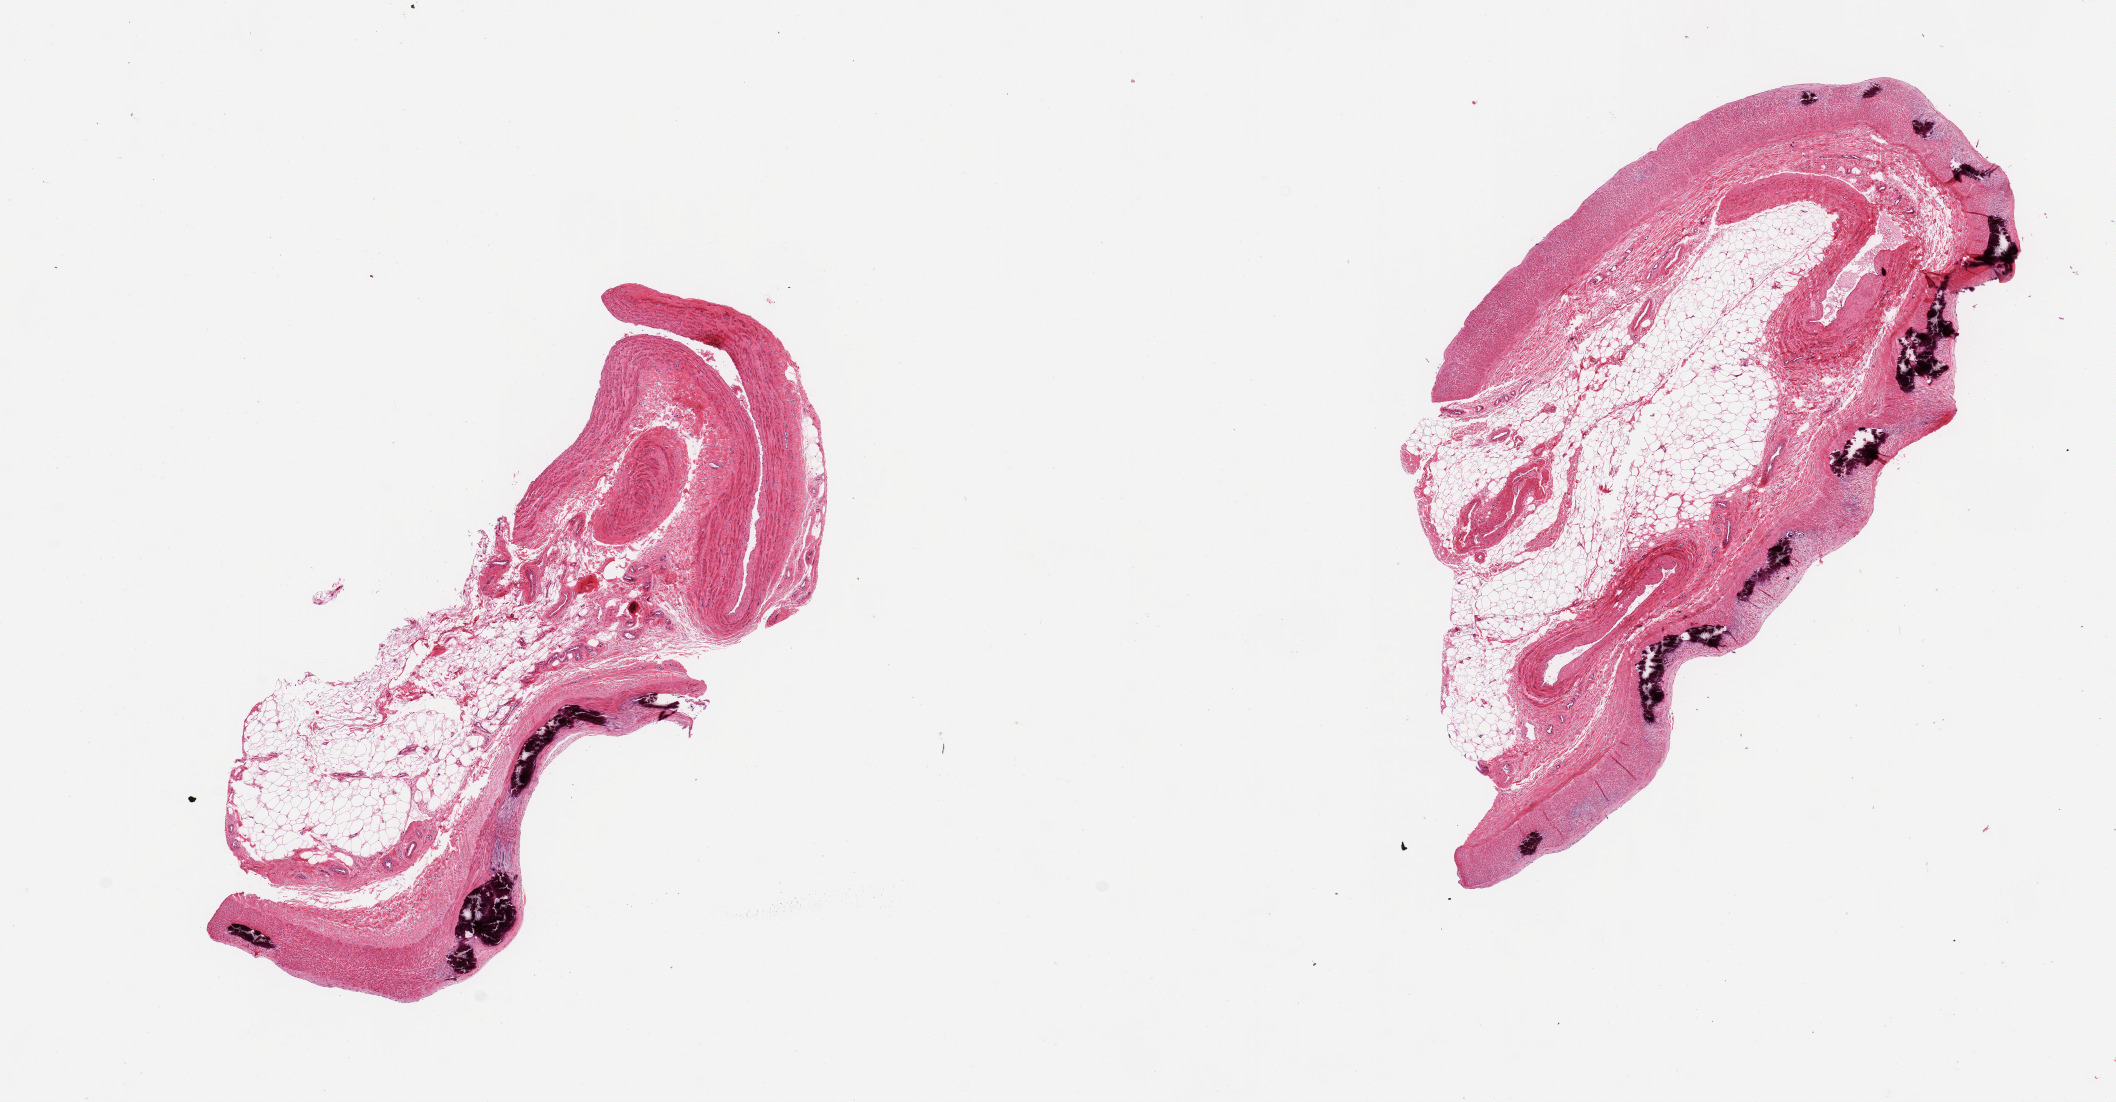
Haematoxylin and eosin whole-slide image, brightfield, low-resolution overview of the scanned area, about 16.7 x 8.7 mm (from a 20x scan). PAXgene-fixed paraffin-embedded (PFPE) section. Section of tibial artery (target tissue). Tissue donor sample. Donor sex: male.
Reviewer comment on this tissue sample: 2 pieces; fragments of vessel wall with significant medial calcification and attachment of fat (30-50%) and vessels.